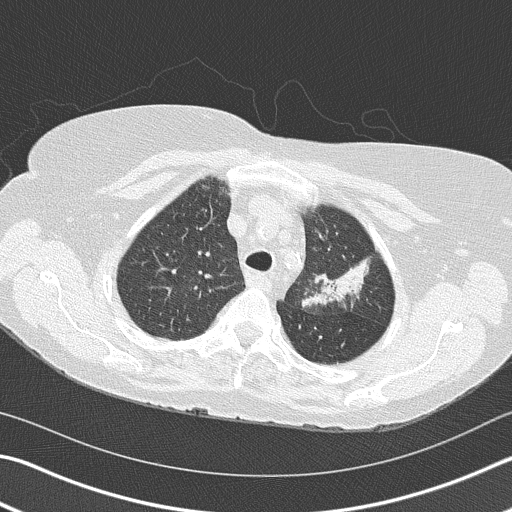
Axial slice from a low-dose chest CT screening exam; second annual screen; lung window (W 1500 / L -600 HU); 2 mm slice thickness; slice 125 of 153 in the series; 512 × 512 image matrix. Female, age 68 years at enrolment.
Expert-annotated lung lesion, box from (x=291, y=224) to (x=379, y=321) px. The exam's reader record, not a measurement of the box and not confirmed to be the same lesion: non-calcified nodule or mass ≥4 mm, left upper lobe, 4 × 2 mm, spiculated (stellate) margins, soft tissue attenuation, pre-existing on the prior screen: yes; interval growth: yes.